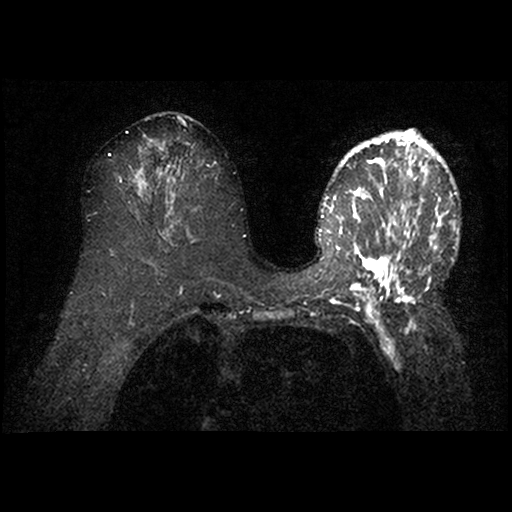
MRI of the breasts; 2 images, each one mid-volume slice chosen by position. Age decade 50s.
Image 1: fluid-sensitive (T2/STIR) axial slice, slice 48 of 95.
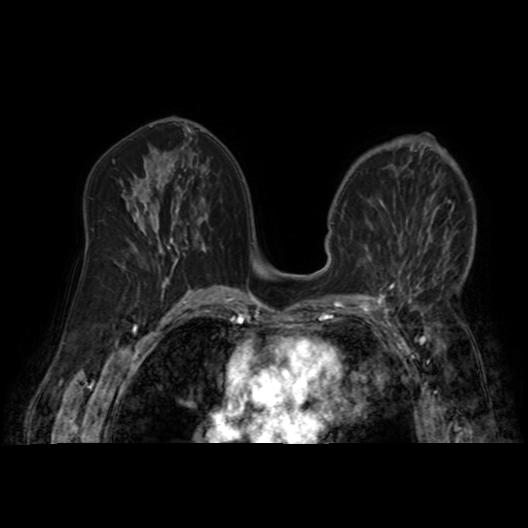
Image 2: post-contrast dynamic axial slice, series "AX BLISS_AUTO SENSE", slice 48 of 95, dynamic phase 5 of 8, 4 mm slice thickness.
Pathology recorded for this patient (not read from these images): pathology diagnosis: Invasive ductal CA (left breast); receptor status (as recorded): ER pos, PR pos (weak), HER2 neg; Ki-67 (as recorded): intermed prolif; pathology report notes: re-bx [date] was scar tissue from RT rx.